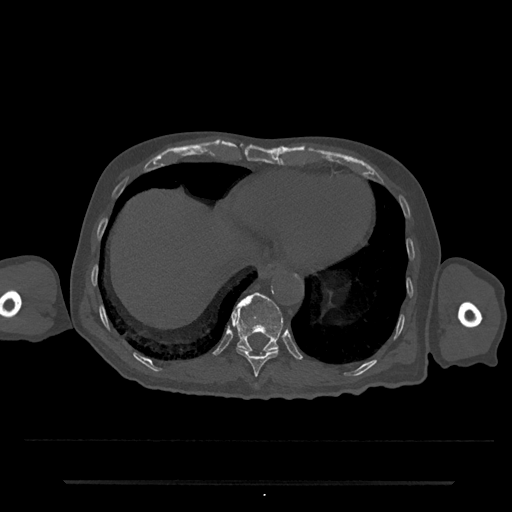
CT including the spine, one axial slice; position 288 of 797 along the scan axis; reconstruction kernel Br40s/3; bone window (W 1800 / L 400 HU); 0.5 mm slice thickness; 512 × 512 image matrix, field of view 427 × 427 mm. Male patient, age 74 years. Case-level facts recorded for this patient, not image findings: primary cancer: prostate.
Outlined on this slice (semi-automatic segmentation, software-assisted and operator-edited):
- T10 vertebra: bounding box (x1, y1, x2, y2) in pixels: (236, 347, 279, 377)
- T11 vertebra: (231, 292, 283, 353)